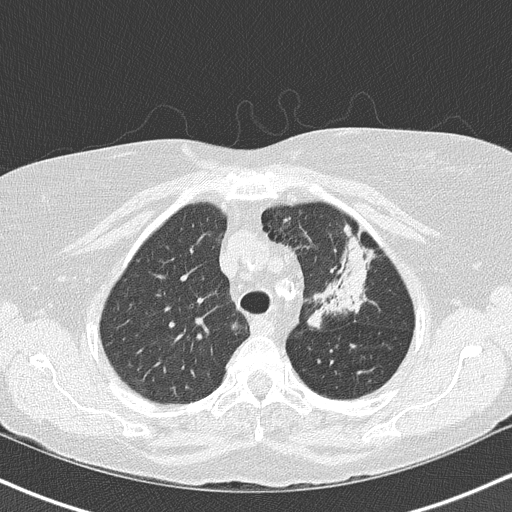
Low-dose screening chest CT, axial slice. Third screening round (two years after baseline). Lung window (W 1500 / L -600 HU). 2 mm slice thickness. Female participant, aged 68 years at enrolment. Former smoker at enrolment.
Expert-annotated lung lesion, bounding box [x1, y1, x2, y2] px = [296, 221, 381, 329]. Reader record for this screening exam (exam-level; its link to the box is not recorded): non-calcified nodule or mass ≥4 mm, left upper lobe, 5 × 5 mm, poorly defined margins, mixed attenuation, pre-existing on the prior screen: yes; interval growth: yes. Official screen result: positive, other. Lung cancer was diagnosed 42 days after this screen: adenocarcinoma, NOS, left upper lobe, poorly differentiated (G3), stage IB (AJCC 6th edition), 50 mm at pathology.